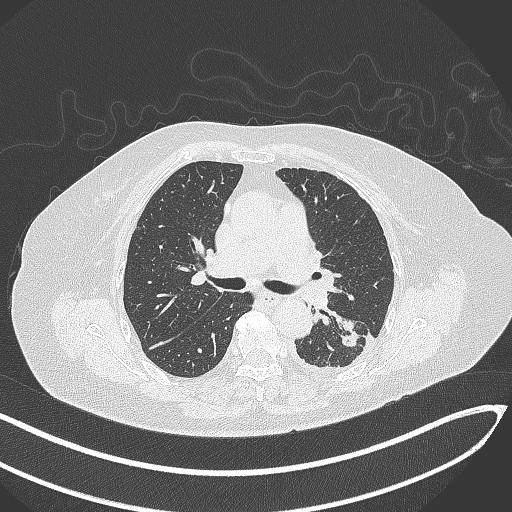
Chest CT, one axial slice; slice 193 of 270 in the series (ordered by position); reconstruction kernel B70f; 120 kVp; lung window (W 1500 / L -600 HU); 1 mm slice thickness; 512 × 512 image matrix, field of view 400 × 400 mm. Female patient, age 76 years. Case-level facts recorded for this patient, not image findings: clinical TNM (as recorded): T1c N0 M0.
Outlined on this slice (bounding box drawn by a radiologist):
- lung tumour (recorded histology: adenocarcinoma): box from (x=335, y=316) to (x=365, y=350) px